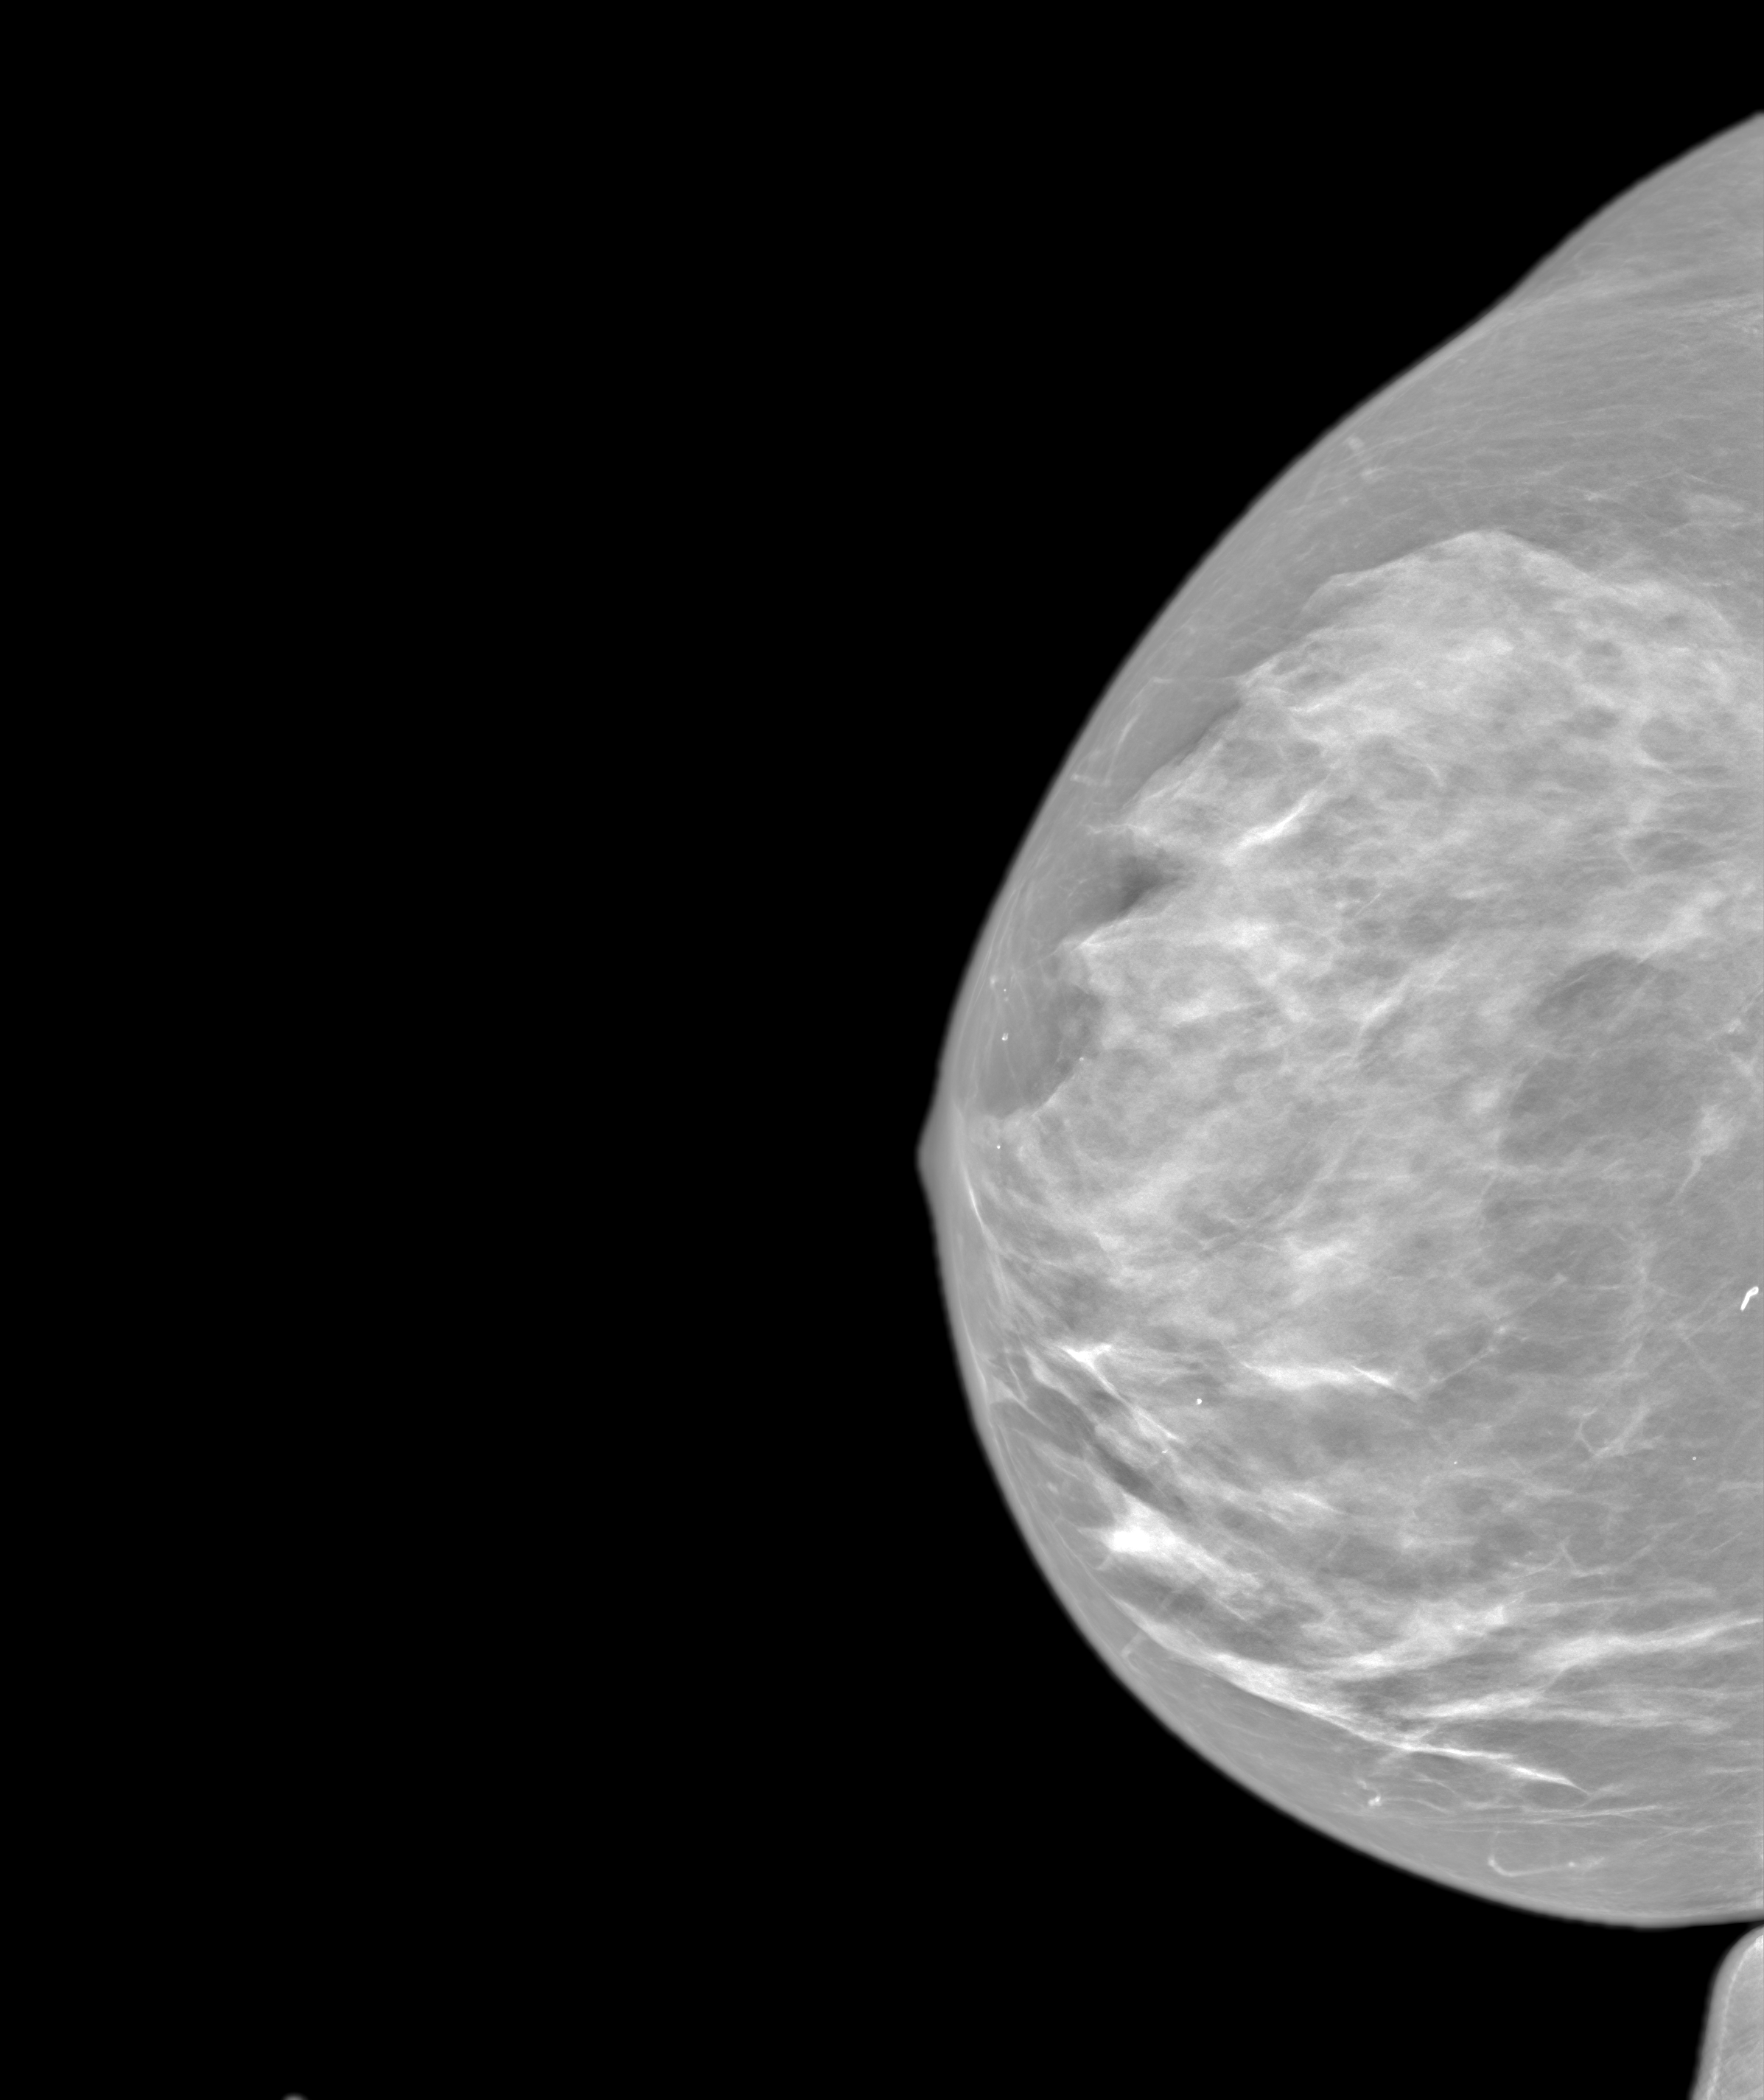
Annual screening mammography examination, system: SenoIris_1SP1.2(425). Female patient, age 65 years.
Image type: synthesized 2-D view from tomosynthesis. Breast: right. Projection: cranio-caudal projection.